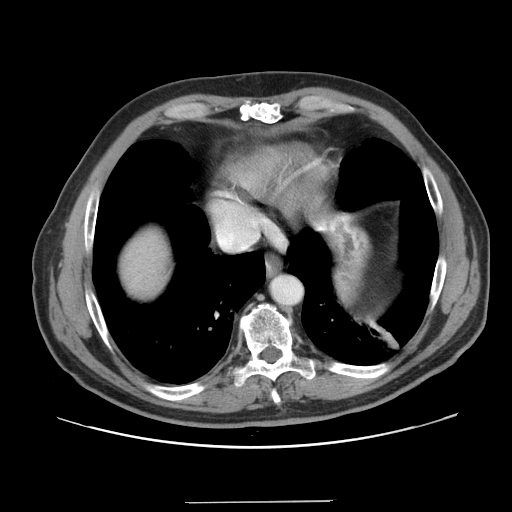
Contrast-enhanced abdominal CT, one axial slice; slice 144 of 151 in the series (ordered by position); 120 kVp; intravenous contrast given; soft-tissue window (W 400 / L 40 HU); 2.5 mm slice thickness; 512 × 512 image matrix, field of view 399 × 399 mm. Male patient, age 63 years. From the clinical record (not read from this slice): diagnosis: colorectal cancer liver metastases, imaged before liver resection; multiple liver metastases: no; largest metastasis: 2.1 cm; disease in both lobes: no.
Annotated regions visible in this slice (expert manual segmentation):
- hepatic veins: bounding box (x1, y1, x2, y2) in pixels: (218, 220, 258, 250)
- liver: (118, 226, 172, 302)
- planned liver remnant (the part of the liver to remain after resection): (119, 227, 171, 303)